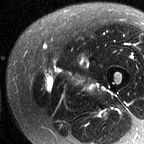
MRI of an extremity soft-tissue mass, one axial slice; position 12 of 60 along the scan axis; T2-weighted fat-saturated; MR volume resampled by the dataset authors to the PET/CT grid (not the native acquisition matrix); 144 × 144 image matrix, field of view 141 × 141 mm. Female patient. Case-level facts recorded for this patient, not image findings: histological type: pleiomorphic leiomyosarcoma; grade: intermediate; site of the primary tumour: left thigh.
Annotated regions visible in this slice (expert contour drawn on MRI and transferred to this co-registered scan by the dataset authors):
- gross tumour volume including surrounding oedema: bounding box [x1, y1, x2, y2] px = [93, 86, 99, 91]